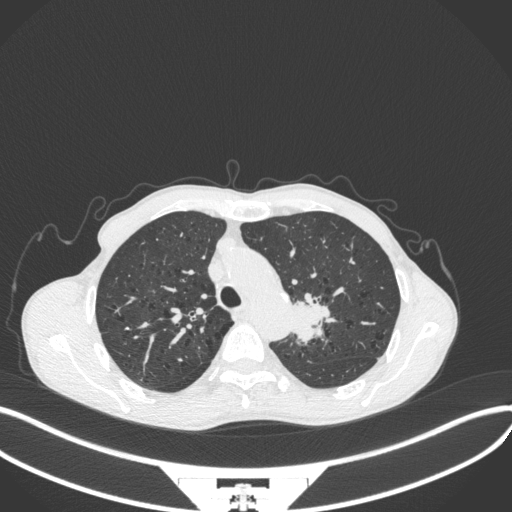
Chest CT, one axial slice. Position 311 of 394 along the scan axis. 120 kVp. Lung window (W 1500 / L -600 HU). 1 mm slice thickness. 512 × 512 image matrix, field of view 400 × 400 mm. Patient: male, 65 years. From the clinical record (not read from this slice): clinical TNM (as recorded): T2b N0 M0; histopathological grade: G2.
Outlined on this slice (rectangle marked by the reading radiologist):
- lung tumour (recorded histology: adenocarcinoma): box from (x=284, y=286) to (x=340, y=348) px